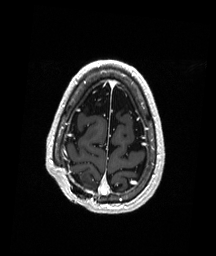
Brain MRI from a brain-tumour surgery series, one axial slice; T1-weighted post-contrast; 1 mm slice thickness; 216 × 256 image matrix, field of view 211 × 250 mm. Case-level facts recorded for this patient, not image findings: histopathology: Astrocytoma; WHO grade: 3; IDH mutation: yes; tumour location: Right Parietal.
Outlined on this slice (manually delineated by an expert):
- previous resection cavity: box from (x=71, y=174) to (x=84, y=185) px